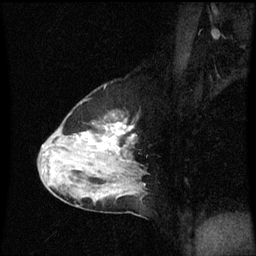
Breast MRI (dynamic contrast-enhanced), one sagittal slice; slice 41 of 60 in the series (ordered by position); dynamic contrast-enhanced series, image 2 of 3 at this slice position (ordered by acquisition); 1.5 T; TE 4.2 ms, TR 8.9 ms; 2 mm slice thickness; 256 × 256 image matrix. Patient: female, 50 years. Case-level facts recorded for this patient, not image findings: setting: breast cancer imaged before/during neoadjuvant chemotherapy; receptor status: HR-positive, HER2-negative.
Structures marked on this image (semi-automatic segmentation, software-assisted and operator-edited):
- analysis volume of interest (the breast-tissue region the enhancement analysis was run in; not a lesion): bounding box (x1, y1, x2, y2) in pixels: (40, 112, 147, 209)
- tumour enhancement mask (voxels above the 70 % enhancement threshold inside the analysis volume of interest): (82, 132, 122, 155)